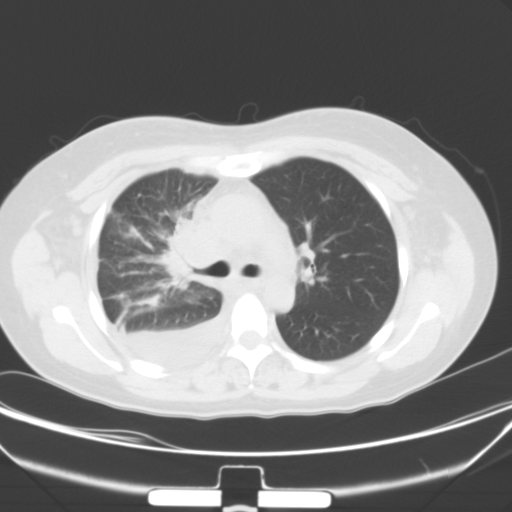
Chest CT, one axial slice; slice 23 of 40 in the series (ordered by position); lung window (W 1500 / L -600 HU); 5 mm slice thickness; 512 × 512 image matrix, field of view 352 × 352 mm. Female patient, age 36 years. From the clinical record (not read from this slice): clinical TNM (as recorded): T1b N2 M0.
Outlined on this slice (bounding box drawn by a radiologist):
- lung tumour (recorded histology: adenocarcinoma): bounding box <151,213,213,298> (left, top, right, bottom; pixels)